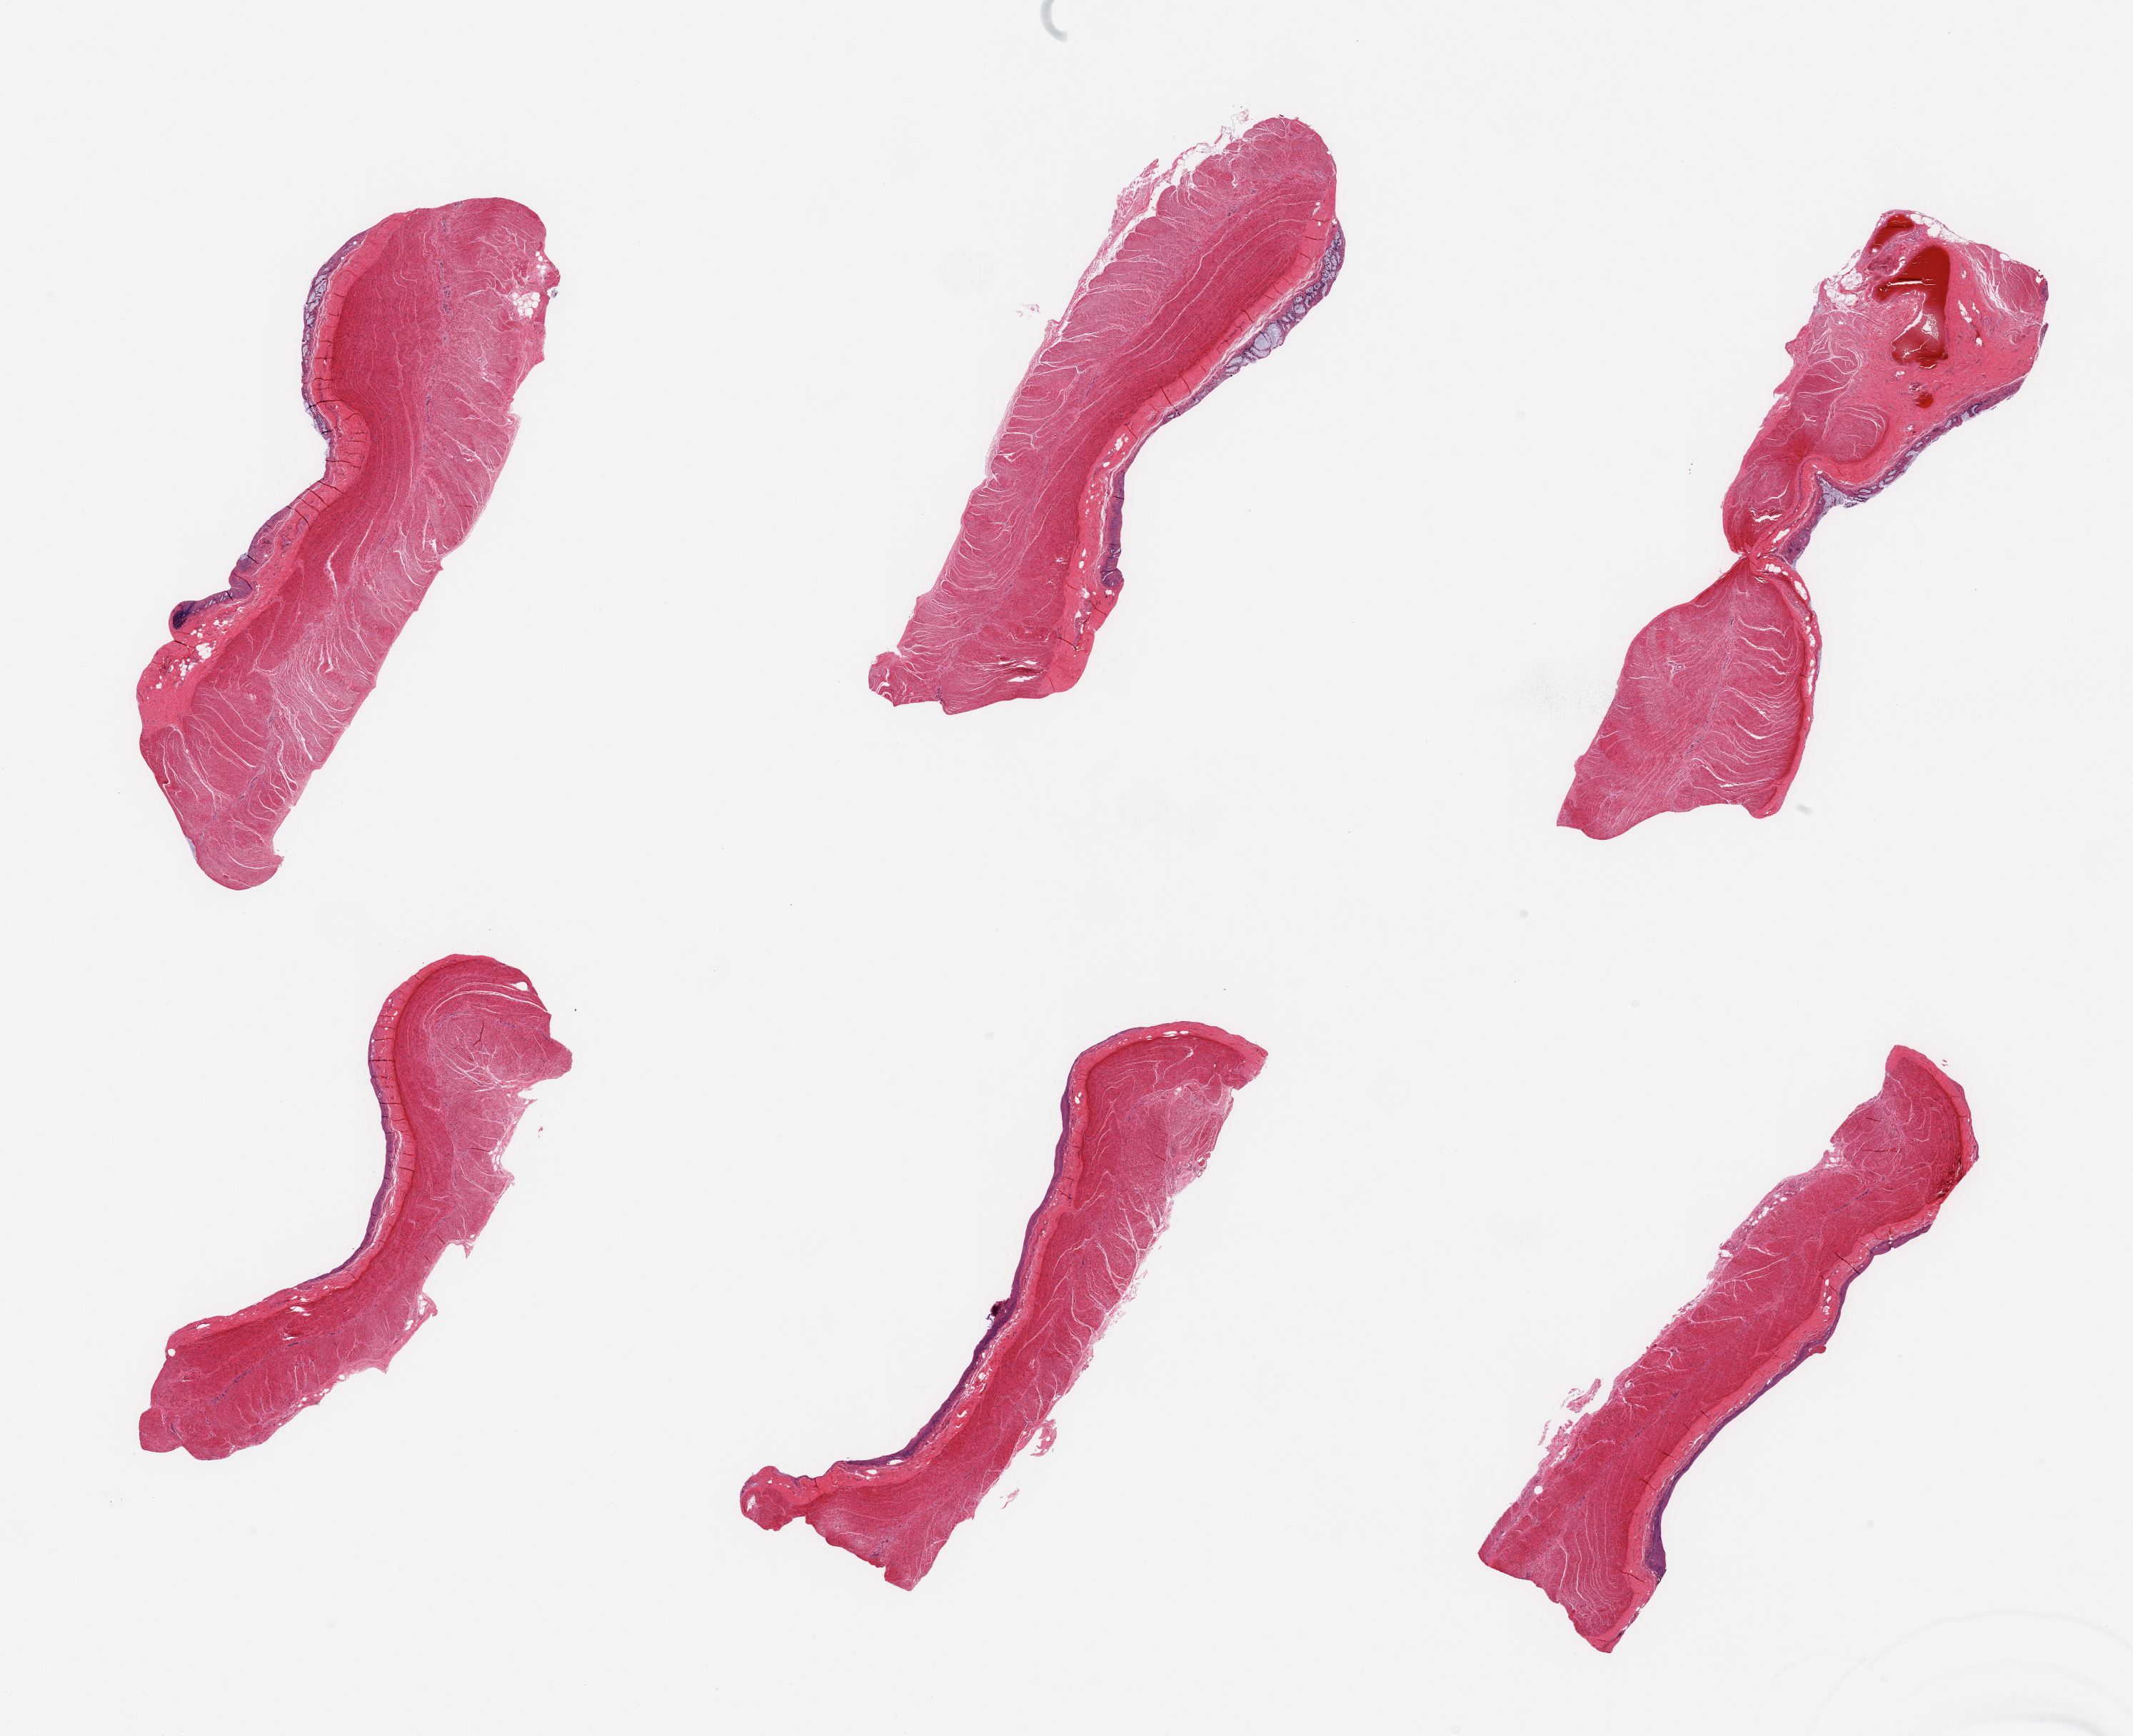
Whole-slide image, H&E stain — shown as a low-resolution overview of the whole scanned area (about 23.6 x 19.2 mm); PAXgene-fixed paraffin-embedded (PFPE) section; section of sigmoid colon (target tissue); donor tissue sample. Donor: female.
- review note (as recorded): 6 pieces; residual autolyzed mucosa on several pieces